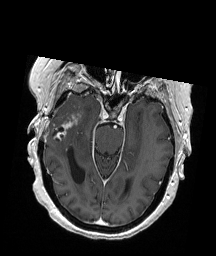
Brain MRI from a brain-tumour surgery series, one axial slice. Position 125 of 192 along the scan axis. T1-weighted post-contrast. 1 mm slice thickness. 216 × 256 image matrix, field of view 211 × 250 mm. From the clinical record (not read from this slice): histopathology: Glioblastoma; WHO grade: 4; IDH mutation: no; tumour location: Right Temporal.
Annotated regions visible in this slice (manually delineated by an expert):
- tumour: bounding box <54,115,80,139> (left, top, right, bottom; pixels)